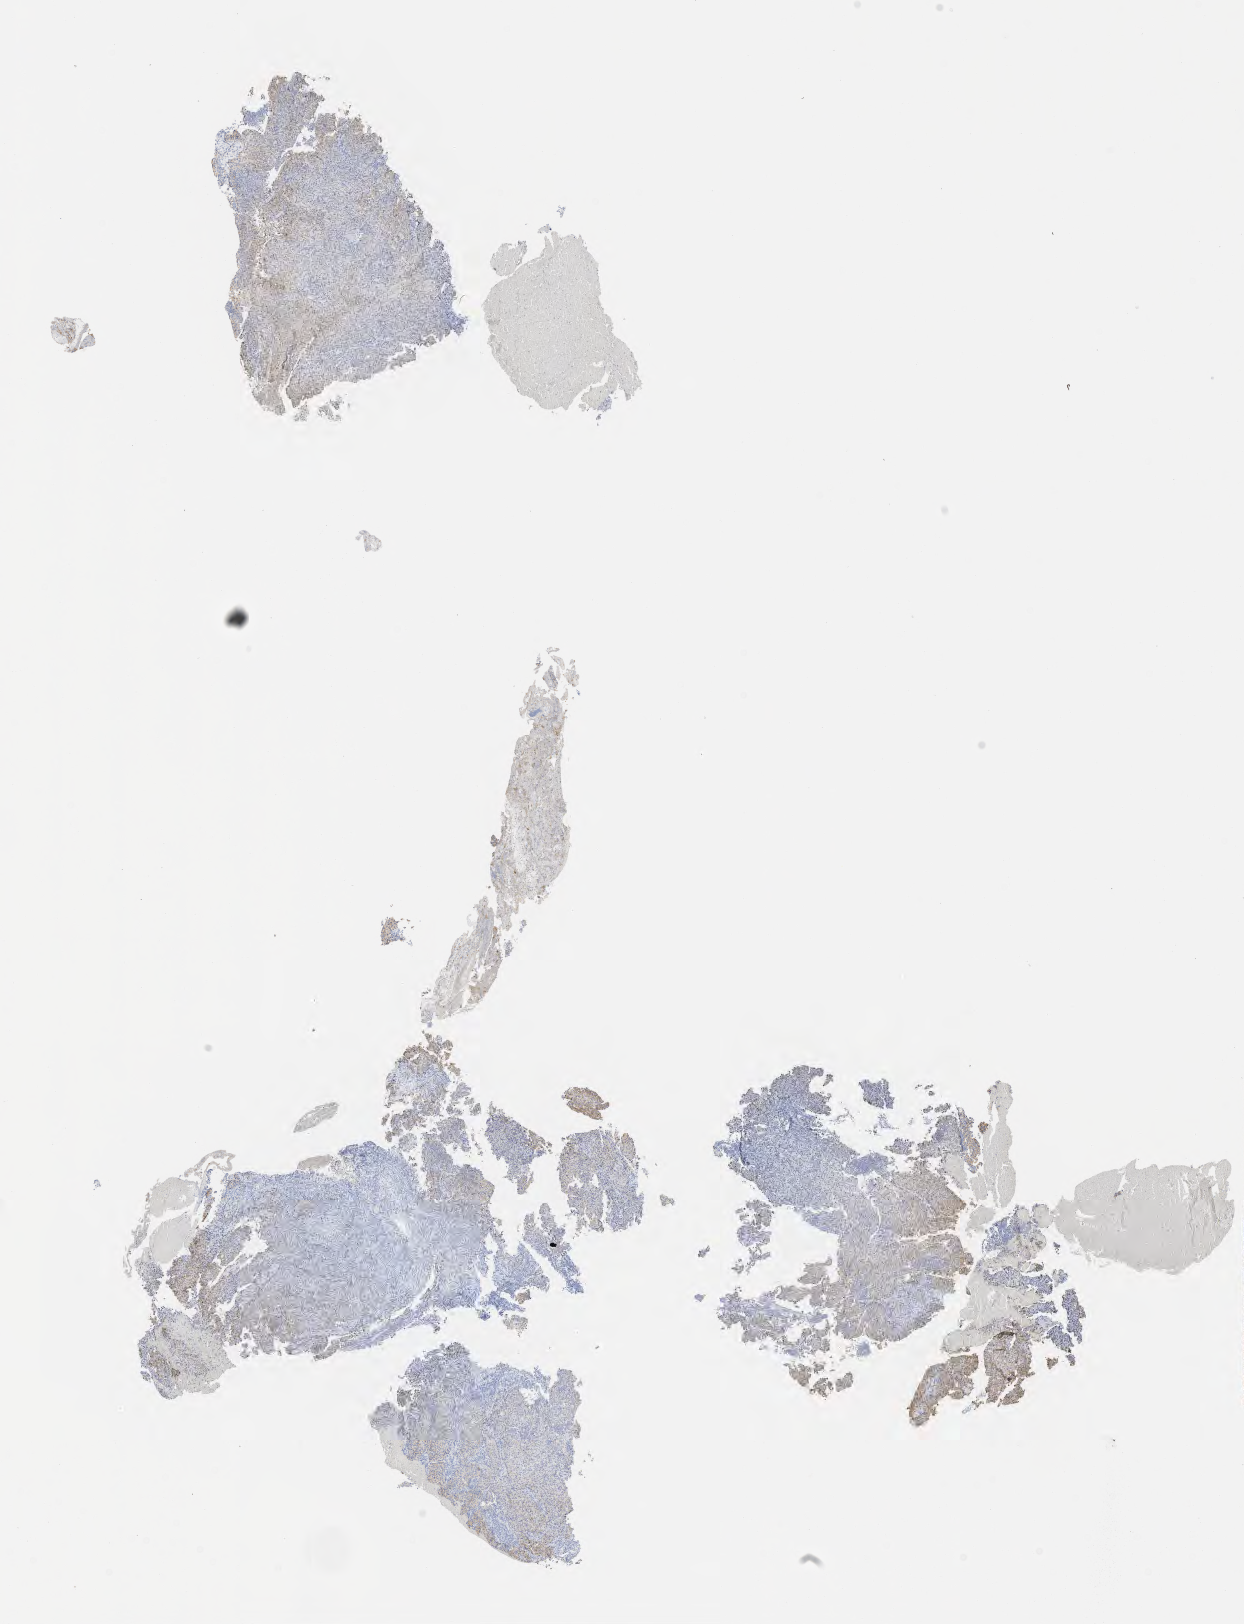
IHC for Ber-EP4, whole-slide image, whole scanned area (about 10.1 x 13.1 mm) shown as a low-resolution overview. Tumor tissue. Anatomic site: cervix. Patient: female, aged 33.
Diagnosis: Squamous cell carcinoma, large cell, nonkeratinizing, NOS.